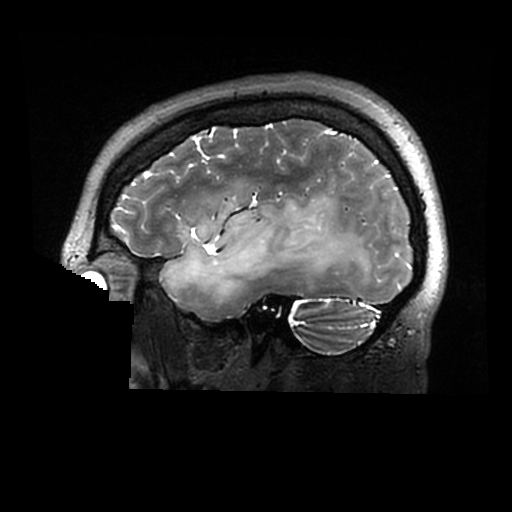
Brain MRI from a brain-tumour surgery series, one sagittal slice. Slice 223 of 320 in the series (ordered by position). 512 × 512 image matrix, field of view 240 × 240 mm. Case-level facts recorded for this patient, not image findings: histopathology: Astrocytoma; WHO grade: 2; IDH mutation: yes.
Structures marked on this image (outlined manually by an expert reader):
- tumour: bounding box <161,194,381,303> (left, top, right, bottom; pixels)